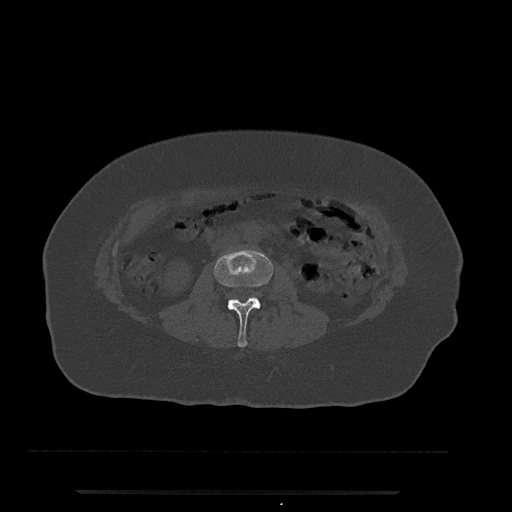
CT including the spine, one axial slice; slice 18 of 797 in the series (ordered by position); reconstruction kernel Br40s/3; 120 kVp; bone window (W 1800 / L 400 HU); 512 × 512 image matrix, field of view 440 × 440 mm. Patient: female, 51 years. From the clinical record (not read from this slice): primary cancer: neuro; vertebrae with lytic lesions (as recorded): T8.
Outlined on this slice (semi-automatic segmentation, software-assisted and operator-edited):
- L2 vertebra: bounding box [x1, y1, x2, y2] px = [214, 248, 273, 347]